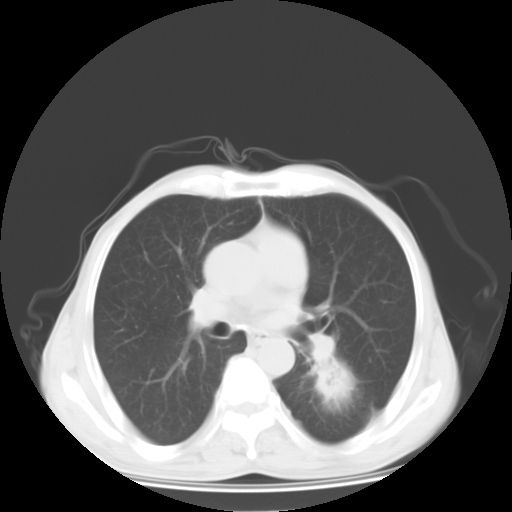
Chest CT, one axial slice; slice 12 of 27 in the series (ordered by position); reconstruction kernel STANDARD; 120 kVp; lung window (W 1500 / L -600 HU); 512 × 512 image matrix. Patient: male, 63 years. Case-level facts recorded for this patient, not image findings: clinical TNM (as recorded): T1c N0 M1b.
Annotated regions visible in this slice (bounding box drawn by a radiologist):
- lung tumour (recorded histology: adenocarcinoma): bounding box (x1, y1, x2, y2) in pixels: (298, 353, 362, 418)